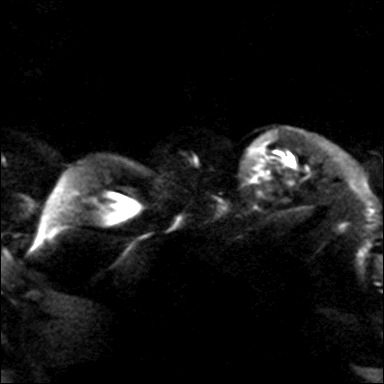
Breast MRI, one axial slice; slice 27 of 40 in the series (ordered by position); diffusion-weighted series; image 2 of 4 stored at this slice position (different b-values; order by instance number); 3 T; 4 mm slice thickness; 384 × 384 image matrix, field of view 320 × 320 mm. Female patient.
Structures marked on this image (outlined manually by an expert reader):
- tumour on diffusion-weighted imaging: bounding box <287,156,294,166> (left, top, right, bottom; pixels)